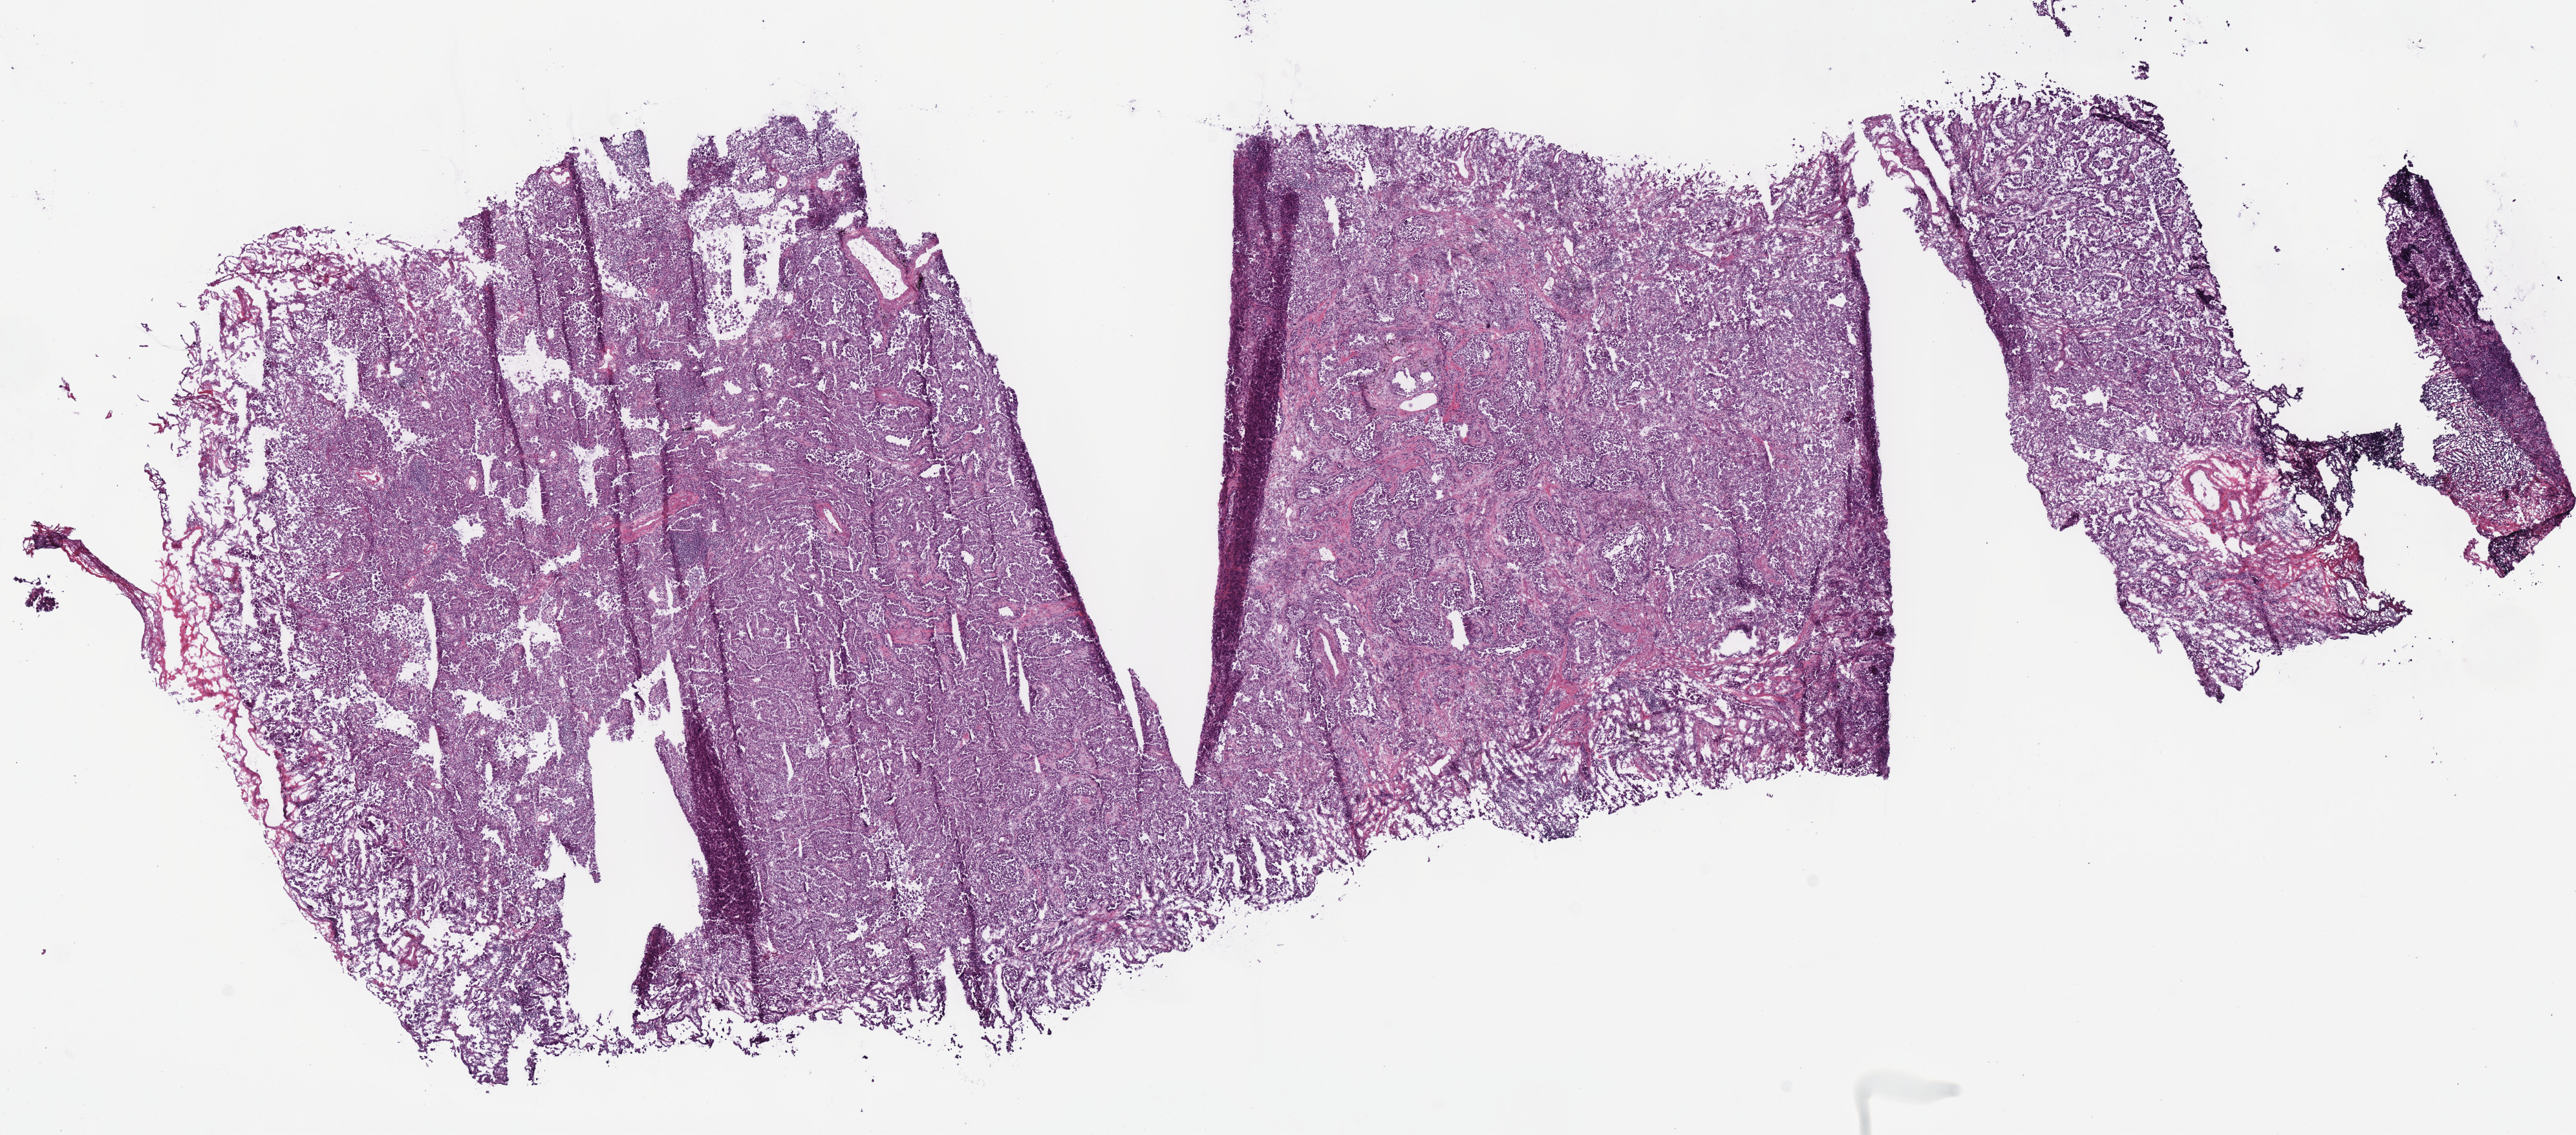
Digitized Hematoxylin and eosin (H&E) stained tissue section (whole slide), low-resolution overview of the scanned area, about 15.7 x 6.9 mm. Frozen section from the top of the tissue portion. Sample: primary tumour, lung. Male, age 75 years at initial diagnosis. Slide review estimates, as recorded: tumour cells 82%, tumour nuclei 85%, normal cells 8%, stromal cells 10%, necrosis 0%.
- TNM: T1 NX M0
- AJCC pathologic stage: IA (7th edition)
- diagnosis: Adenocarcinoma, NOS (lower lobe, lung)